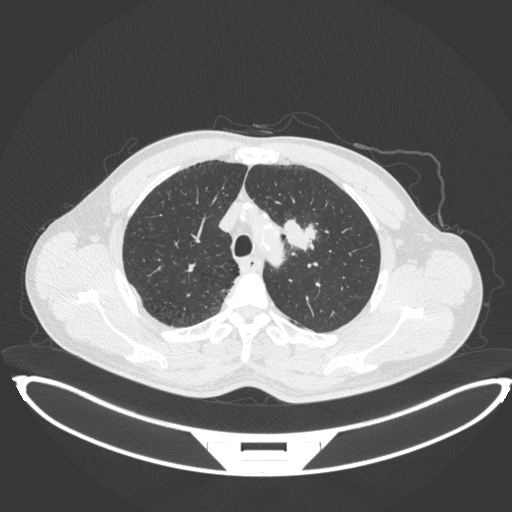
Chest CT, one axial slice; slice 338 of 407 in the series (ordered by position); lung window (W 1500 / L -600 HU); 1 mm slice thickness; 512 × 512 image matrix, field of view 457 × 457 mm. Male patient, age 60 years. Case-level facts recorded for this patient, not image findings: clinical TNM (as recorded): T2a N0 M0.
Outlined on this slice (bounding box drawn by a radiologist):
- lung tumour (recorded histology: squamous cell carcinoma): box from (x=280, y=212) to (x=321, y=253) px